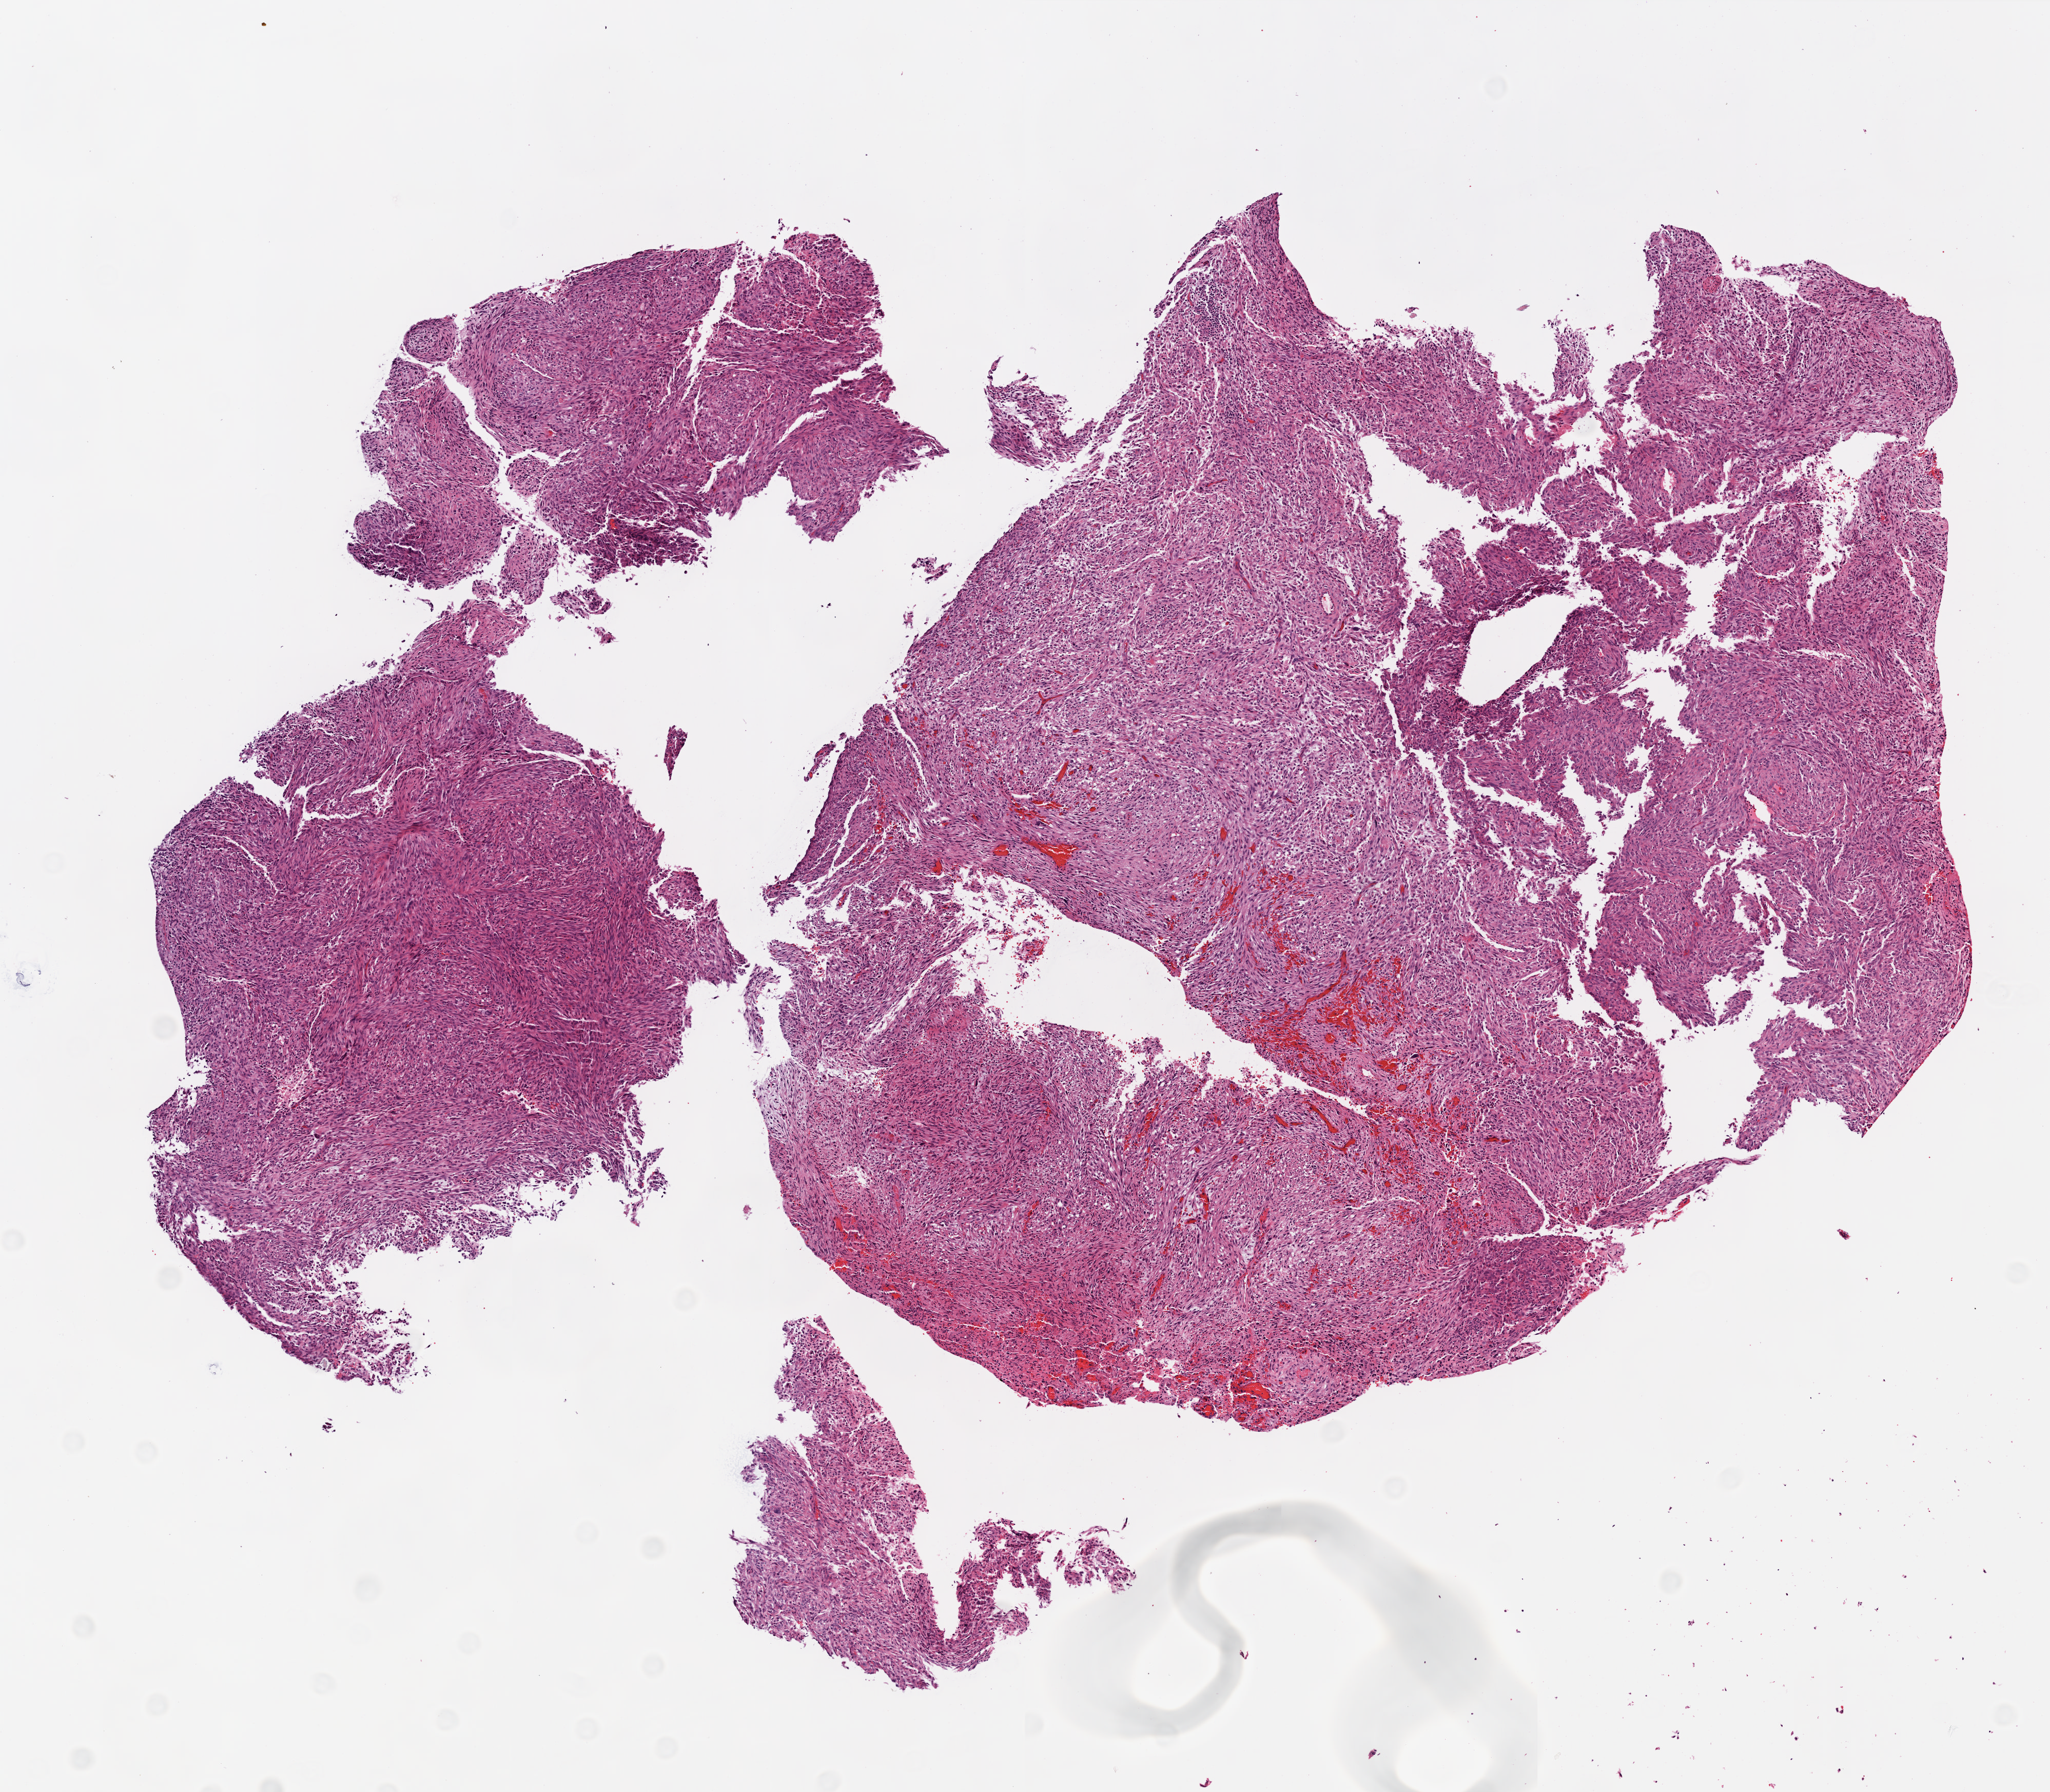
Whole-slide histology image, H&E — shown as a low-resolution overview of the whole scanned area (about 8.0 x 7.0 mm, acquisition: 20x scan). FFPE section. Primary tumour sample from the brain. Patient: male, age at initial diagnosis 40 years.
Diagnosis: Glioblastoma.